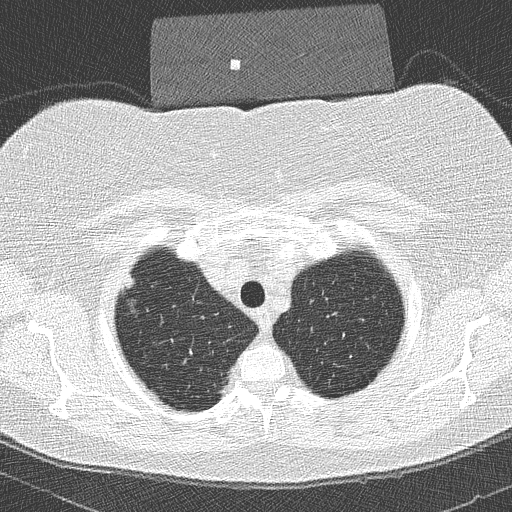
Low-dose screening chest CT, axial slice, second screening round (one year after baseline), lung window (W 1500 / L -600 HU), 512 × 512 image matrix, field of view 320 × 320 mm. Female participant, aged 58 years at enrolment. Former smoker at enrolment.
Expert reader's lesion annotation, bounding box (x1, y1, x2, y2) in pixels: (111, 269, 148, 314). The screening reader recorded 2 non-calcified nodules or masses ≥4 mm on this exam (right upper lobe, right upper lobe); which of them this box marks is not recorded.